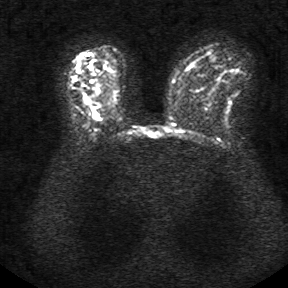
Breast MRI, one axial slice; position 23 of 34 along the scan axis; diffusion-weighted series; image 2 of 4 stored at this slice position (different b-values; order by instance number); 1.5 T; 288 × 288 image matrix. Female patient.
Structures marked on this image (expert manual segmentation):
- tumour on diffusion-weighted imaging: bounding box (x1, y1, x2, y2) in pixels: (92, 109, 98, 116)